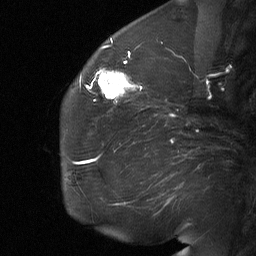
Breast MRI (dynamic contrast-enhanced), one sagittal slice; slice 22 of 64 in the series (ordered by position); dynamic contrast-enhanced study with each time point stored as its own series, time point 2 of 3 at this slice position (early post-contrast, ordered by acquisition time); 1.5 T; TE 4.8 ms, TR 27 ms; 256 × 256 image matrix. Patient: female, 60 years. From the clinical record (not read from this slice): setting: breast cancer imaged before/during neoadjuvant chemotherapy; receptor status: HR-positive, HER2-negative.
Outlined on this slice (semi-automatic segmentation, software-assisted and operator-edited):
- analysis volume of interest (the breast-tissue region the enhancement analysis was run in; not a lesion): bounding box [x1, y1, x2, y2] px = [91, 56, 139, 104]
- tumour enhancement mask (voxels above the 90 % enhancement threshold inside the analysis volume of interest): [95, 68, 137, 99]